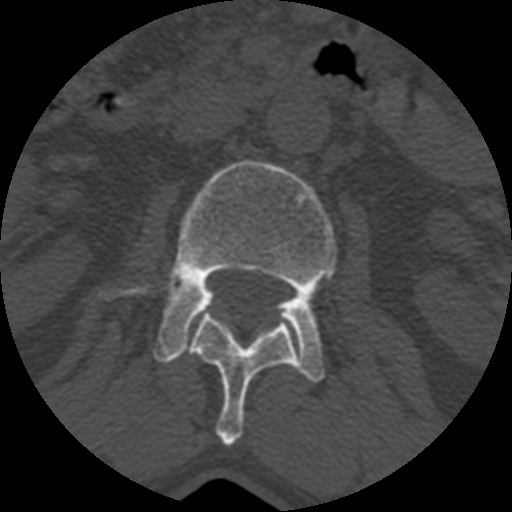
CT including the spine, one axial slice; position 344 of 399 along the scan axis; bone window (W 1800 / L 400 HU); 1.25 mm slice thickness; 512 × 512 image matrix, field of view 160 × 160 mm. Patient age 71 years. Case-level facts recorded for this patient, not image findings: primary cancer: prostate.
Outlined on this slice (semi-automatically segmented with operator editing):
- L1 vertebra: bounding box (x1, y1, x2, y2) in pixels: (187, 313, 297, 446)
- L2 vertebra: (99, 160, 337, 382)